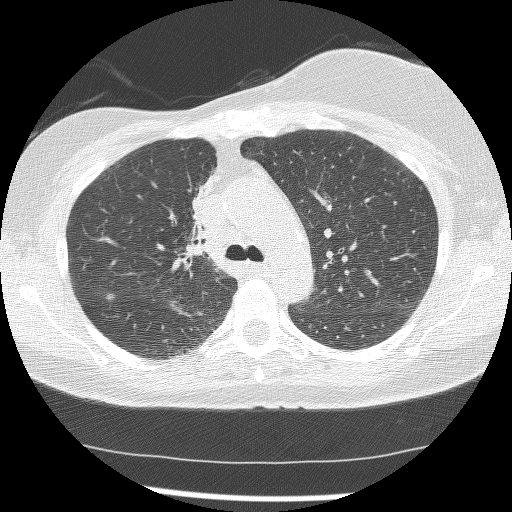
Chest CT (low-dose screening protocol), one axial image, baseline annual screen, lung window (W 1500 / L -600 HU), 2.5 mm slice thickness, lung (sharp) reconstruction kernel (BONE), 120 kVp, slice 49 of 172 in the series, 512 × 512 image matrix, field of view 315 × 315 mm. Female, age 56 years at enrolment. Current smoker at enrolment.
Expert reader's lesion annotation, bounding box (x1, y1, x2, y2) in pixels: (163, 172, 220, 266). The screening reader recorded 2 non-calcified nodules or masses ≥4 mm on this exam (right lower lobe, right middle lobe); which of them this box marks is not recorded. Official screen result: positive, change unspecified: nodule(s) >= 4 mm or enlarging nodule(s), mass(es), or other non-specific abnormalities suspicious for lung cancer. Lung cancer was diagnosed 1185 days after this screen: adenocarcinoma, NOS, right upper lobe, stage IIIB (AJCC 6th edition), 8 mm at pathology.